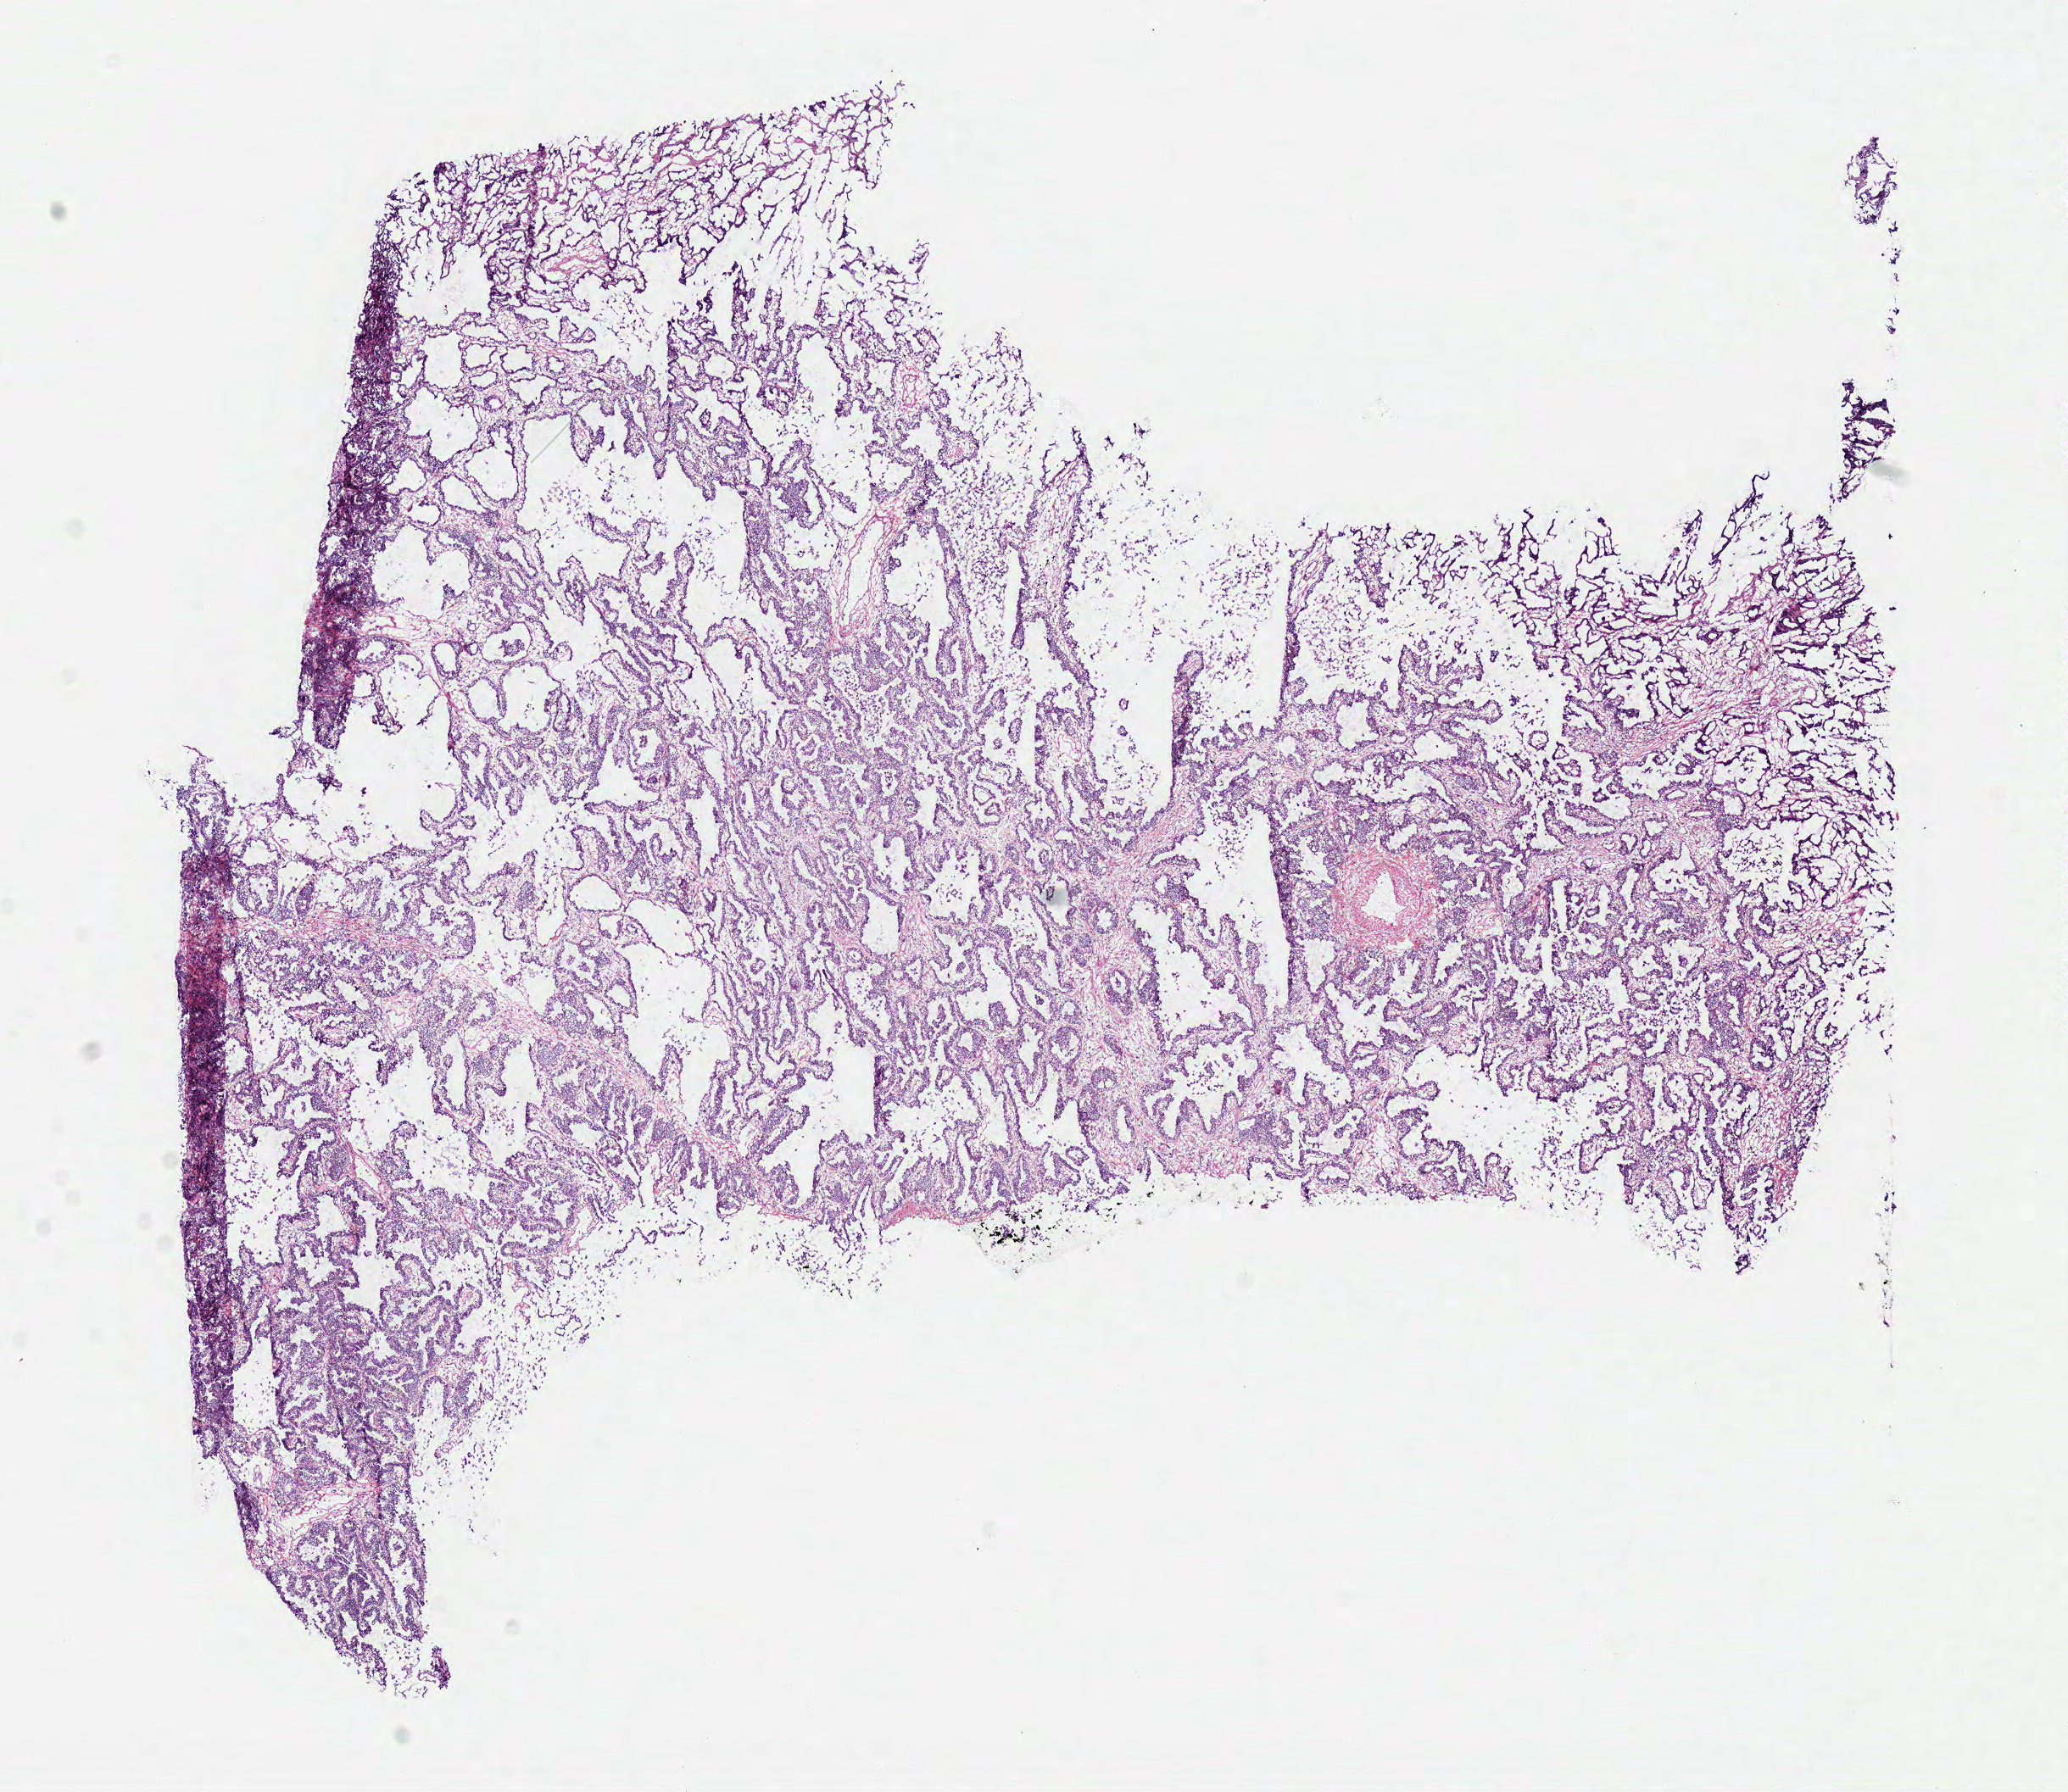
H&E-stained whole-slide image — a low-resolution overview of the entire scanned area, about 9.6 x 8.3 mm (acquisition: 40x scan); frozen section from the top of the tissue portion; primary tumour sample from the lung. Patient: female, age at initial diagnosis 69 years. Slide review estimates, as recorded: tumour cells 90%, tumour nuclei 80%, normal cells 0%, stromal cells 10%, necrosis 0%.
- AJCC pathologic stage: IIB
- histologic diagnosis: Adenocarcinoma with mixed subtypes (upper lobe, lung)
- TNM: T3 N0 M0